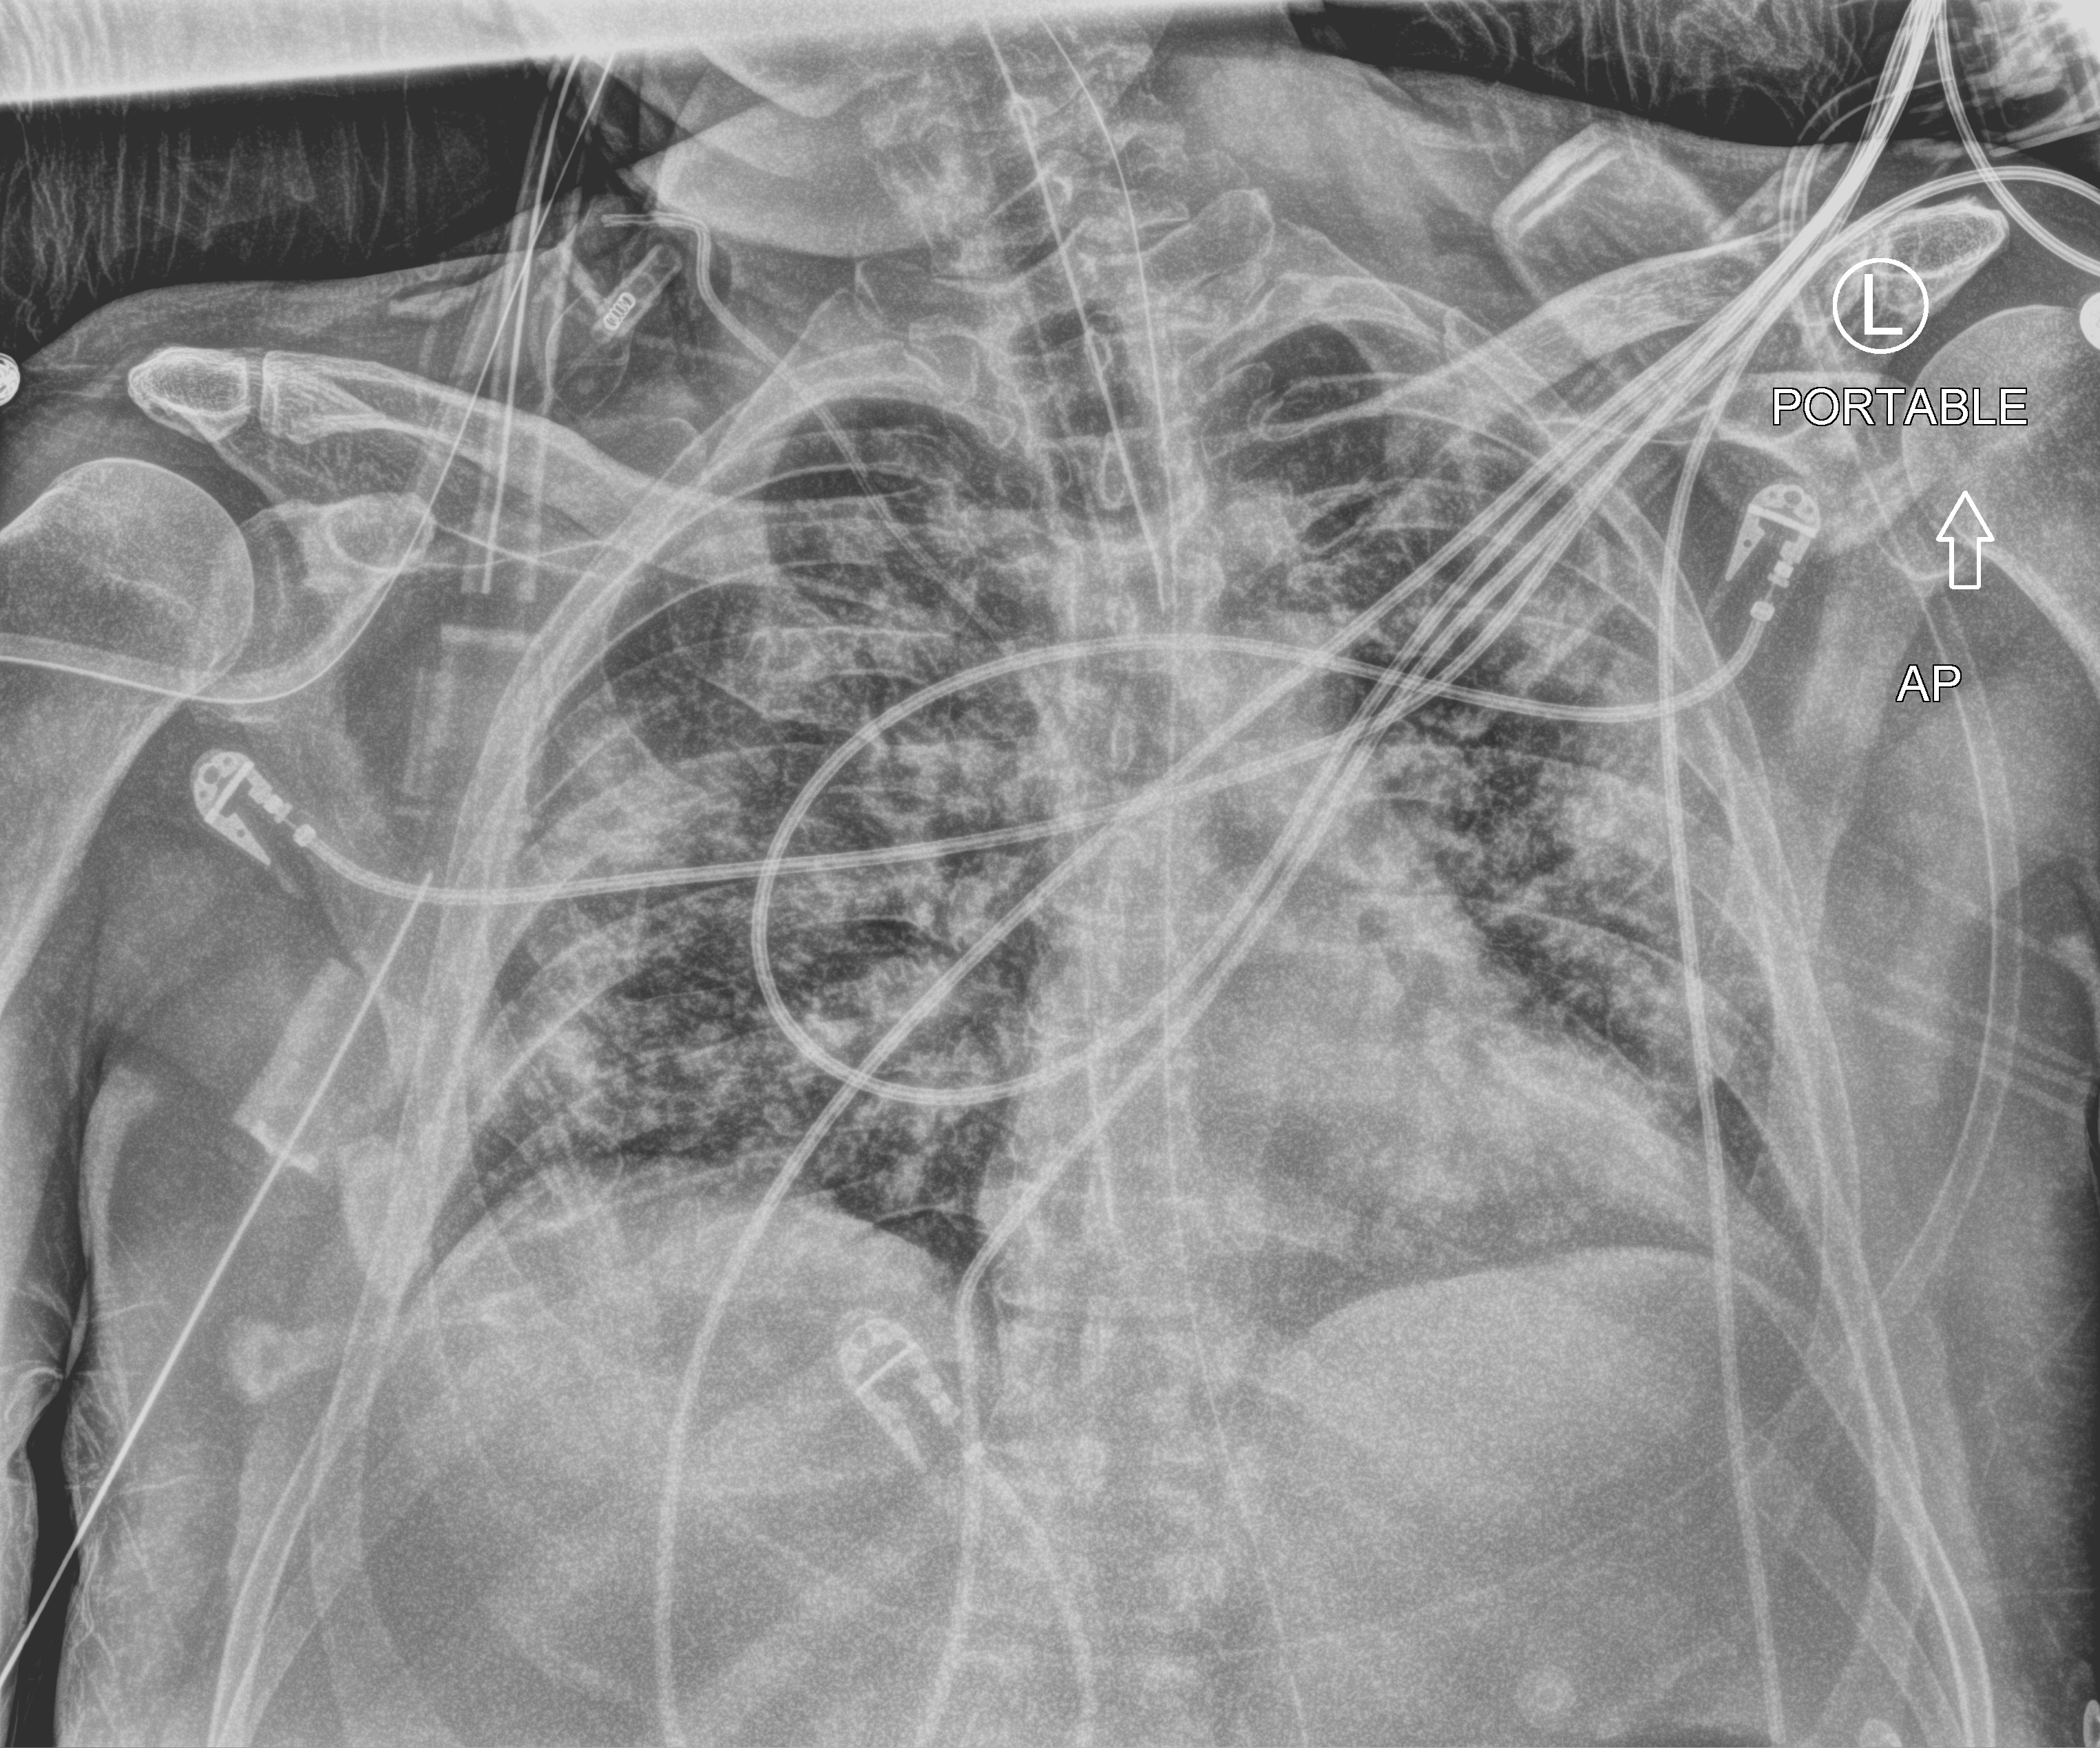
Portable chest radiograph, anteroposterior (AP) projection. Male patient hospitalised with COVID-19, age 18–59 years.
From the hospital-stay record, not from the radiograph (when in the stay this image was taken is not recorded): admitted to intensive care during this hospital stay: yes; mechanically ventilated during this hospital stay: yes.